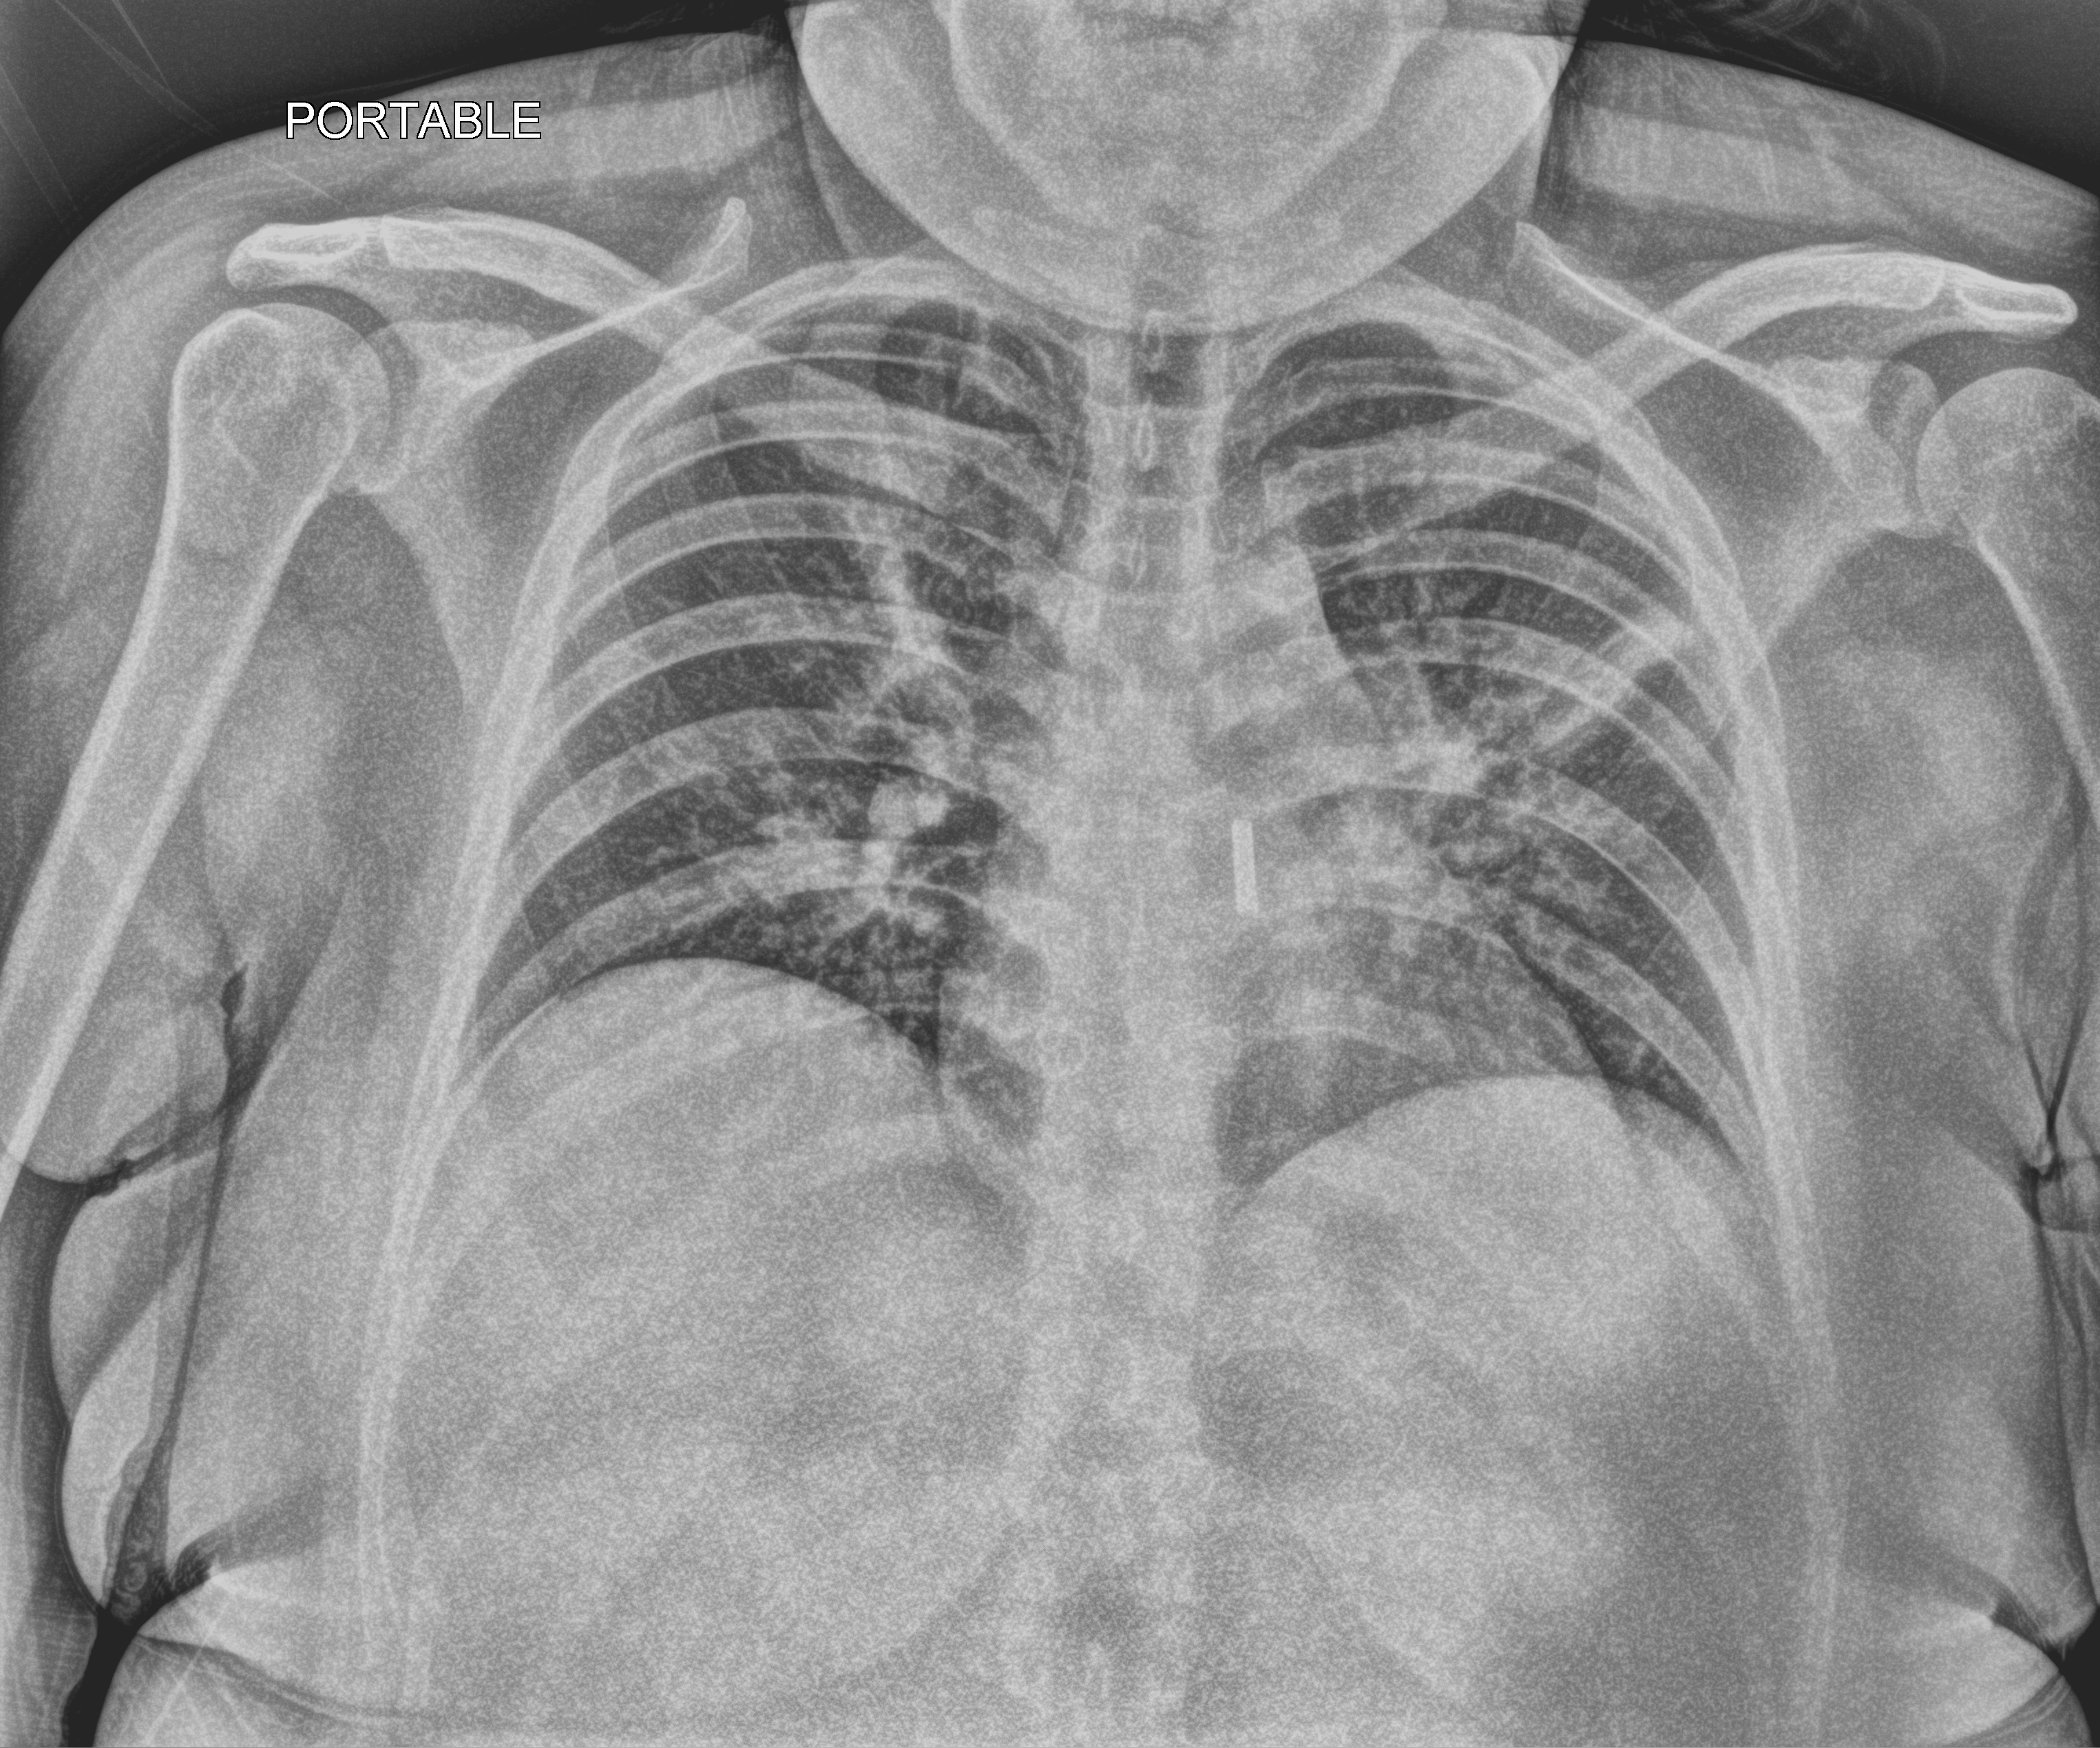
Portable chest radiograph. Female patient hospitalised with COVID-19, age 18–59 years.
Hospital-stay facts (about this admission, not read from this image; timing relative to this image not recorded):
- smoking status (admission record): never